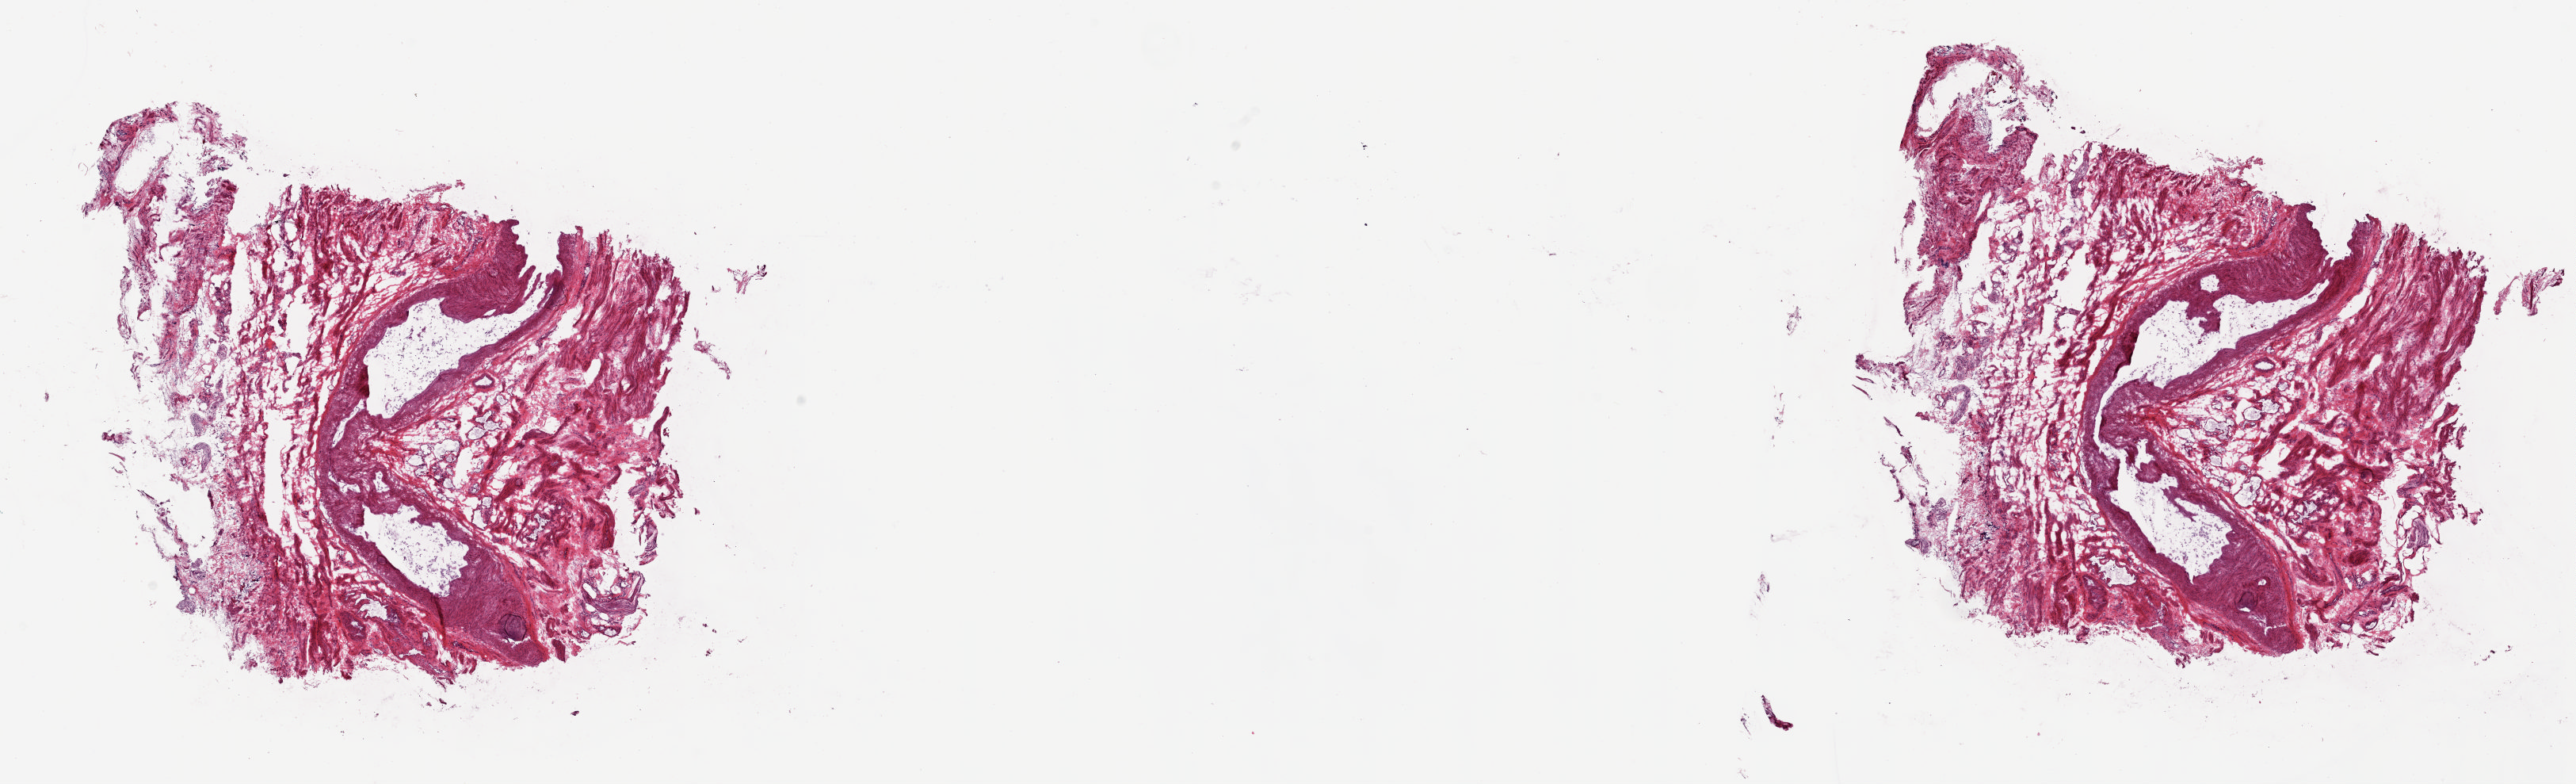
Digitized Hematoxylin and eosin (H&E) stained tissue section (whole slide), whole scanned area (about 25.8 x 7.8 mm) shown as a low-resolution overview. Frozen section. Sample: solid tissue normal (non-tumour tissue), uterus. Female, age 62 years at initial diagnosis. Composition of this section per pathologist review: tumour cells 0%, tumour nuclei 0%, normal cells 100%, stromal cells 0%, necrosis 0%. Infiltration values recorded for this section: lymphocyte infiltration 1%, monocyte infiltration 0%, neutrophil infiltration 0%.
This section: solid tissue normal sample (biorepository sample class). Patient diagnosis: Endometrioid adenocarcinoma, NOS (endometrium).